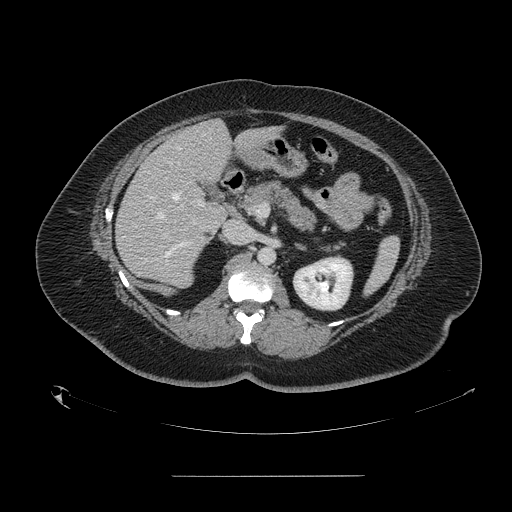
Contrast-enhanced abdominal CT, one axial slice; slice 80 of 164 in the series (ordered by position); 120 kVp; intravenous contrast given; soft-tissue window (W 400 / L 40 HU); 512 × 512 image matrix, field of view 495 × 495 mm. Female patient, age 52 years. Case-level facts recorded for this patient, not image findings: diagnosis: colorectal cancer liver metastases, imaged before liver resection; multiple liver metastases: yes; largest metastasis: 3.5 cm.
Structures marked on this image (outlined manually by an expert reader):
- hepatic veins: box from (x=156, y=133) to (x=203, y=219) px
- liver: (x=117, y=121)–(x=252, y=287)
- planned liver remnant (the part of the liver to remain after resection): (x=177, y=121)–(x=229, y=180)
- portal vein (with intrahepatic branches): (x=163, y=178)–(x=204, y=237)
- liver metastasis: (x=204, y=231)–(x=215, y=240)